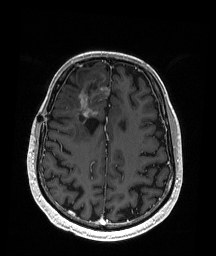
Brain MRI from a brain-tumour surgery series, one axial slice; position 66 of 192 along the scan axis; T1-weighted post-contrast; 216 × 256 image matrix, field of view 211 × 250 mm. Case-level facts recorded for this patient, not image findings: histopathology: Astrocytoma; WHO grade: 3; IDH mutation: yes; tumour location: Right Frontal.
Annotated regions visible in this slice (outlined manually by an expert reader):
- previous resection cavity: bounding box <80,83,98,122> (left, top, right, bottom; pixels)
- tumour: <79,82,109,117>